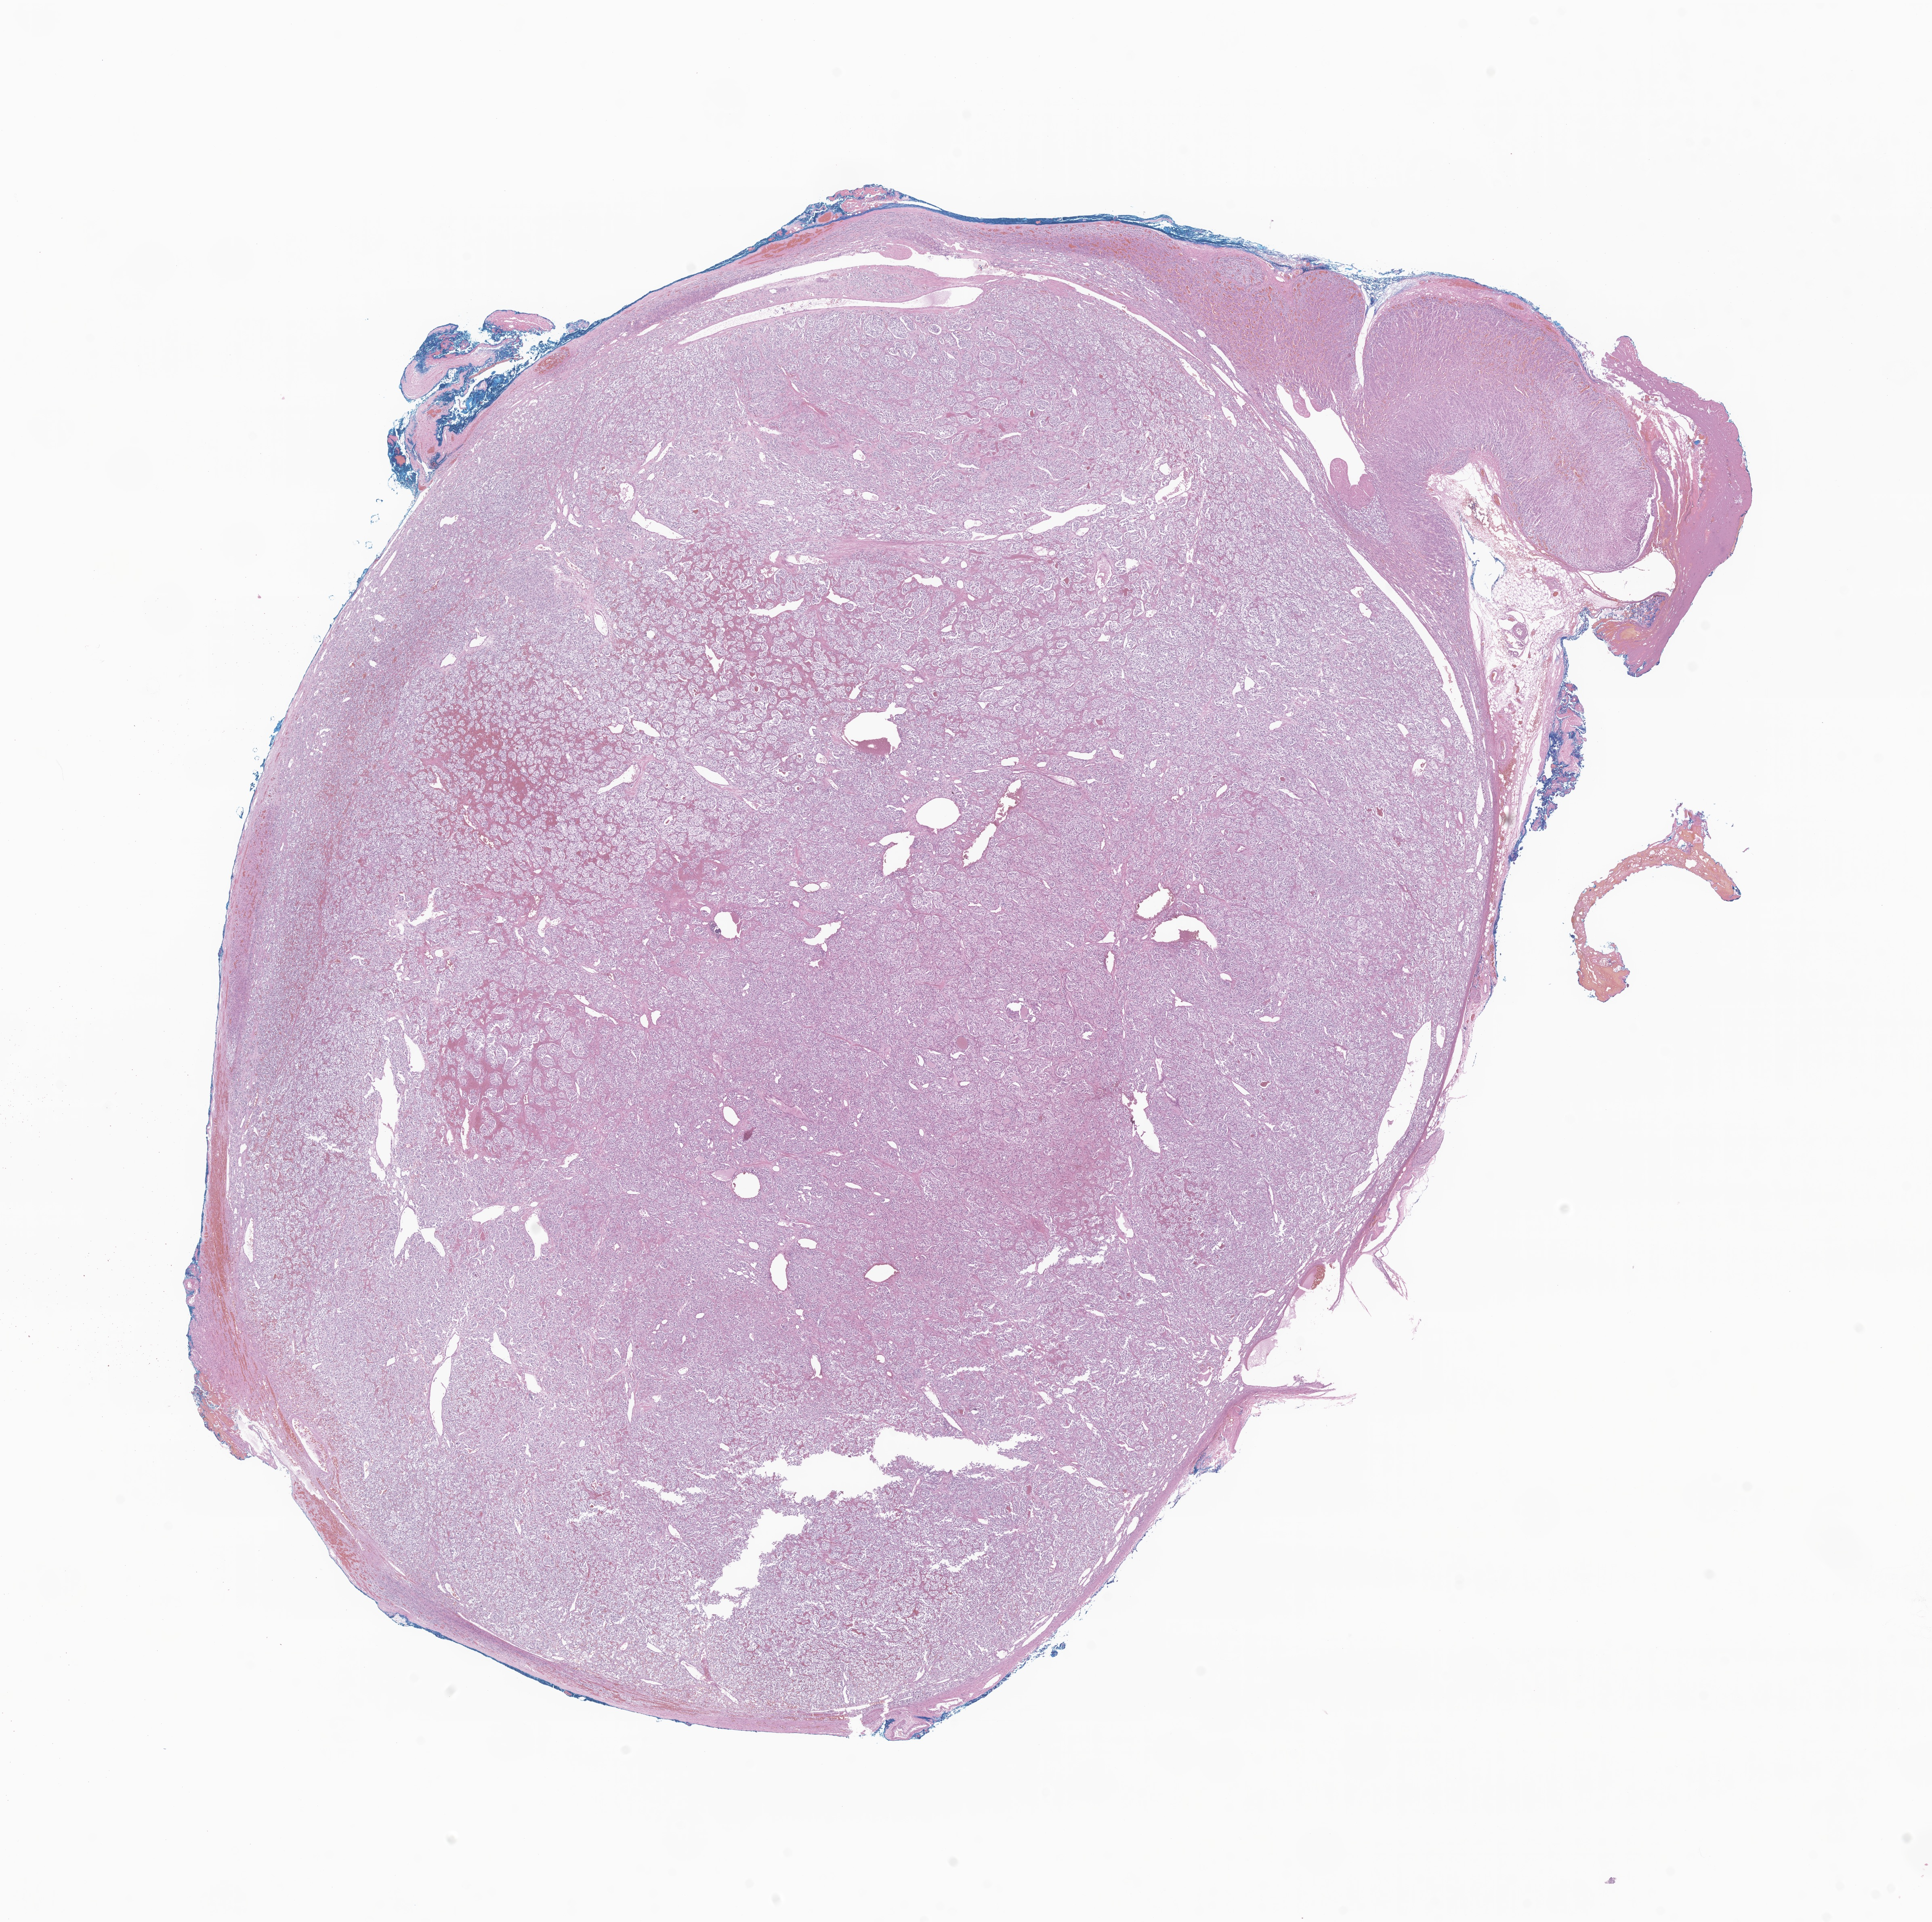
H&E whole-slide image of tumor tissue from the adrenal medulla — low-resolution overview of the scanned area, about 20.2 x 20.1 mm. FFPE section. Patient: female, age 172 months (14 years 4 months).
- recorded diagnosis: Pheochromocytoma, NOS